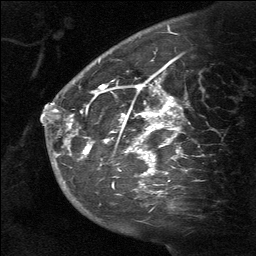
Breast MRI (dynamic contrast-enhanced), one sagittal slice; slice 45 of 64 in the series (ordered by position); dynamic contrast-enhanced study with each time point stored as its own series, time point 2 of 3 at this slice position (early post-contrast, ordered by acquisition time); 1.5 T; TE 4.8 ms, TR 27 ms; 2 mm slice thickness; 256 × 256 image matrix. Patient: female, 39 years. From the clinical record (not read from this slice): setting: breast cancer imaged before/during neoadjuvant chemotherapy; receptor status: HER2-positive.
Annotated regions visible in this slice (semi-automatic segmentation, software-assisted and operator-edited):
- analysis volume of interest (the breast-tissue region the enhancement analysis was run in; not a lesion): bounding box (x1, y1, x2, y2) in pixels: (58, 40, 200, 217)
- tumour enhancement mask (voxels above the 90 % enhancement threshold inside the analysis volume of interest): (69, 81, 180, 194)